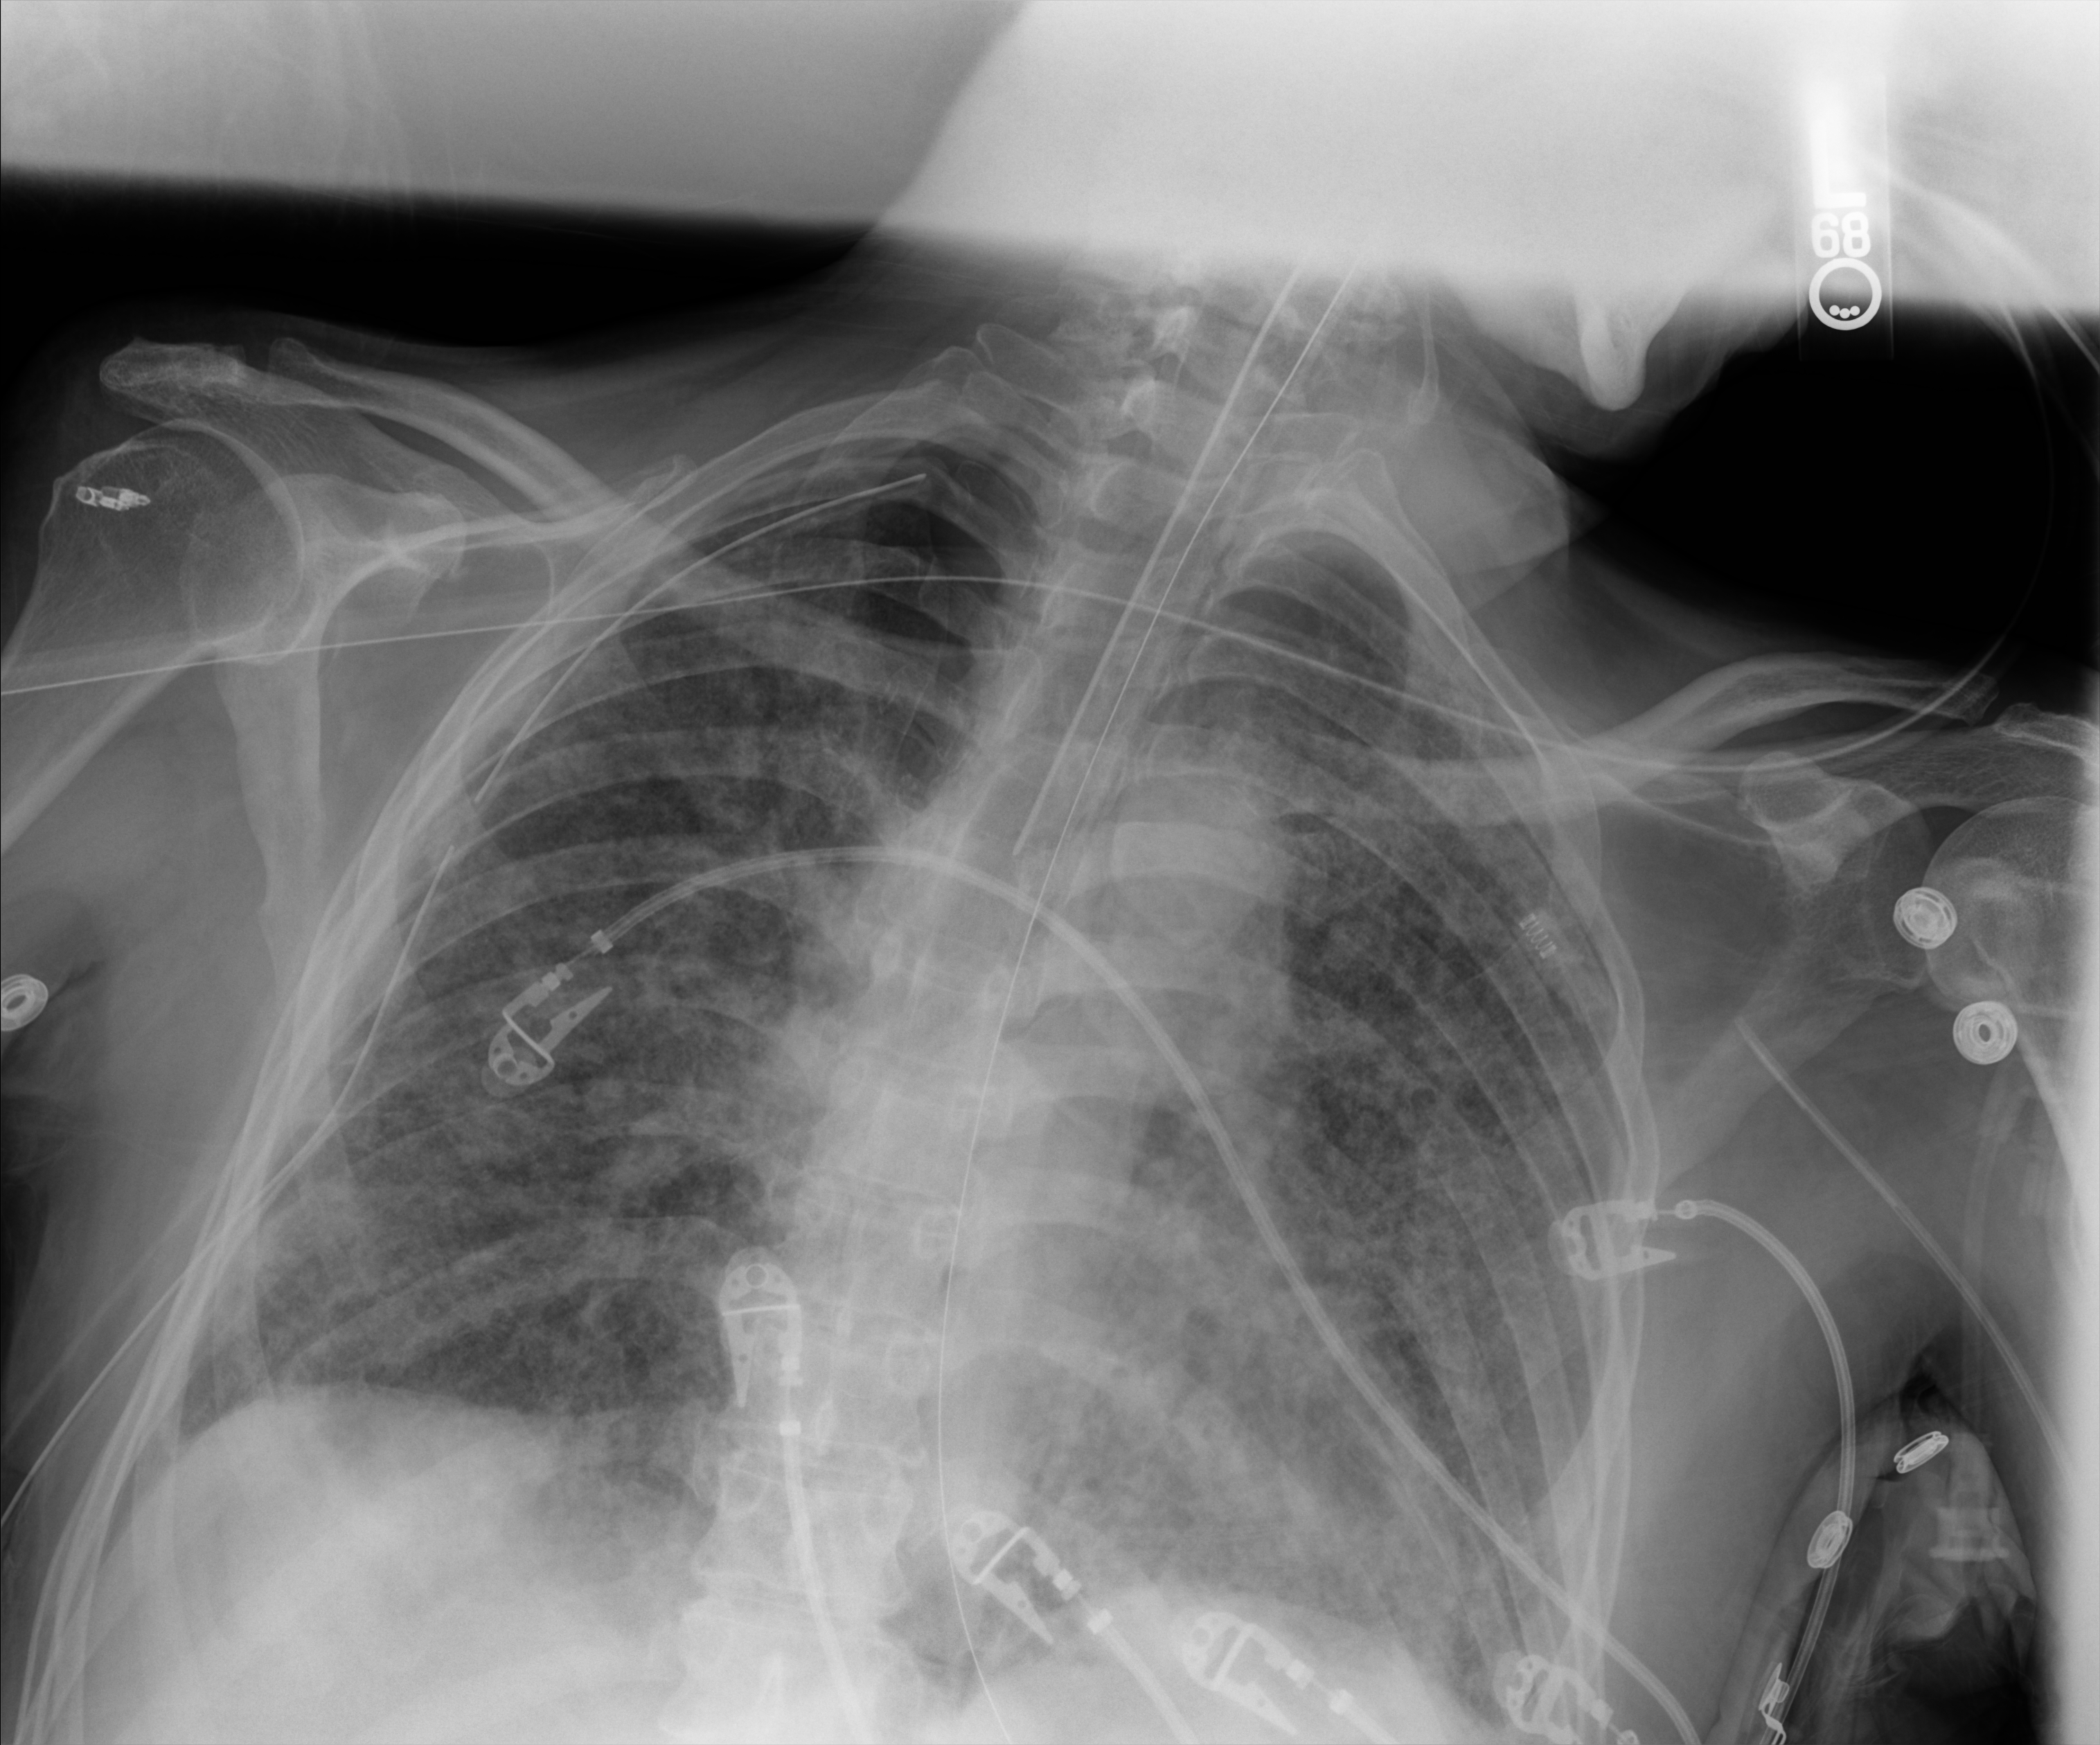
Portable chest radiograph; anteroposterior (AP) projection. Patient hospitalised with COVID-19; male, aged 60–74 years.
From the hospital-stay record, not from the radiograph (when in the stay this image was taken is not recorded): mechanically ventilated during this hospital stay: yes; admitted to intensive care during this hospital stay: yes; hypertension (admission record): no.